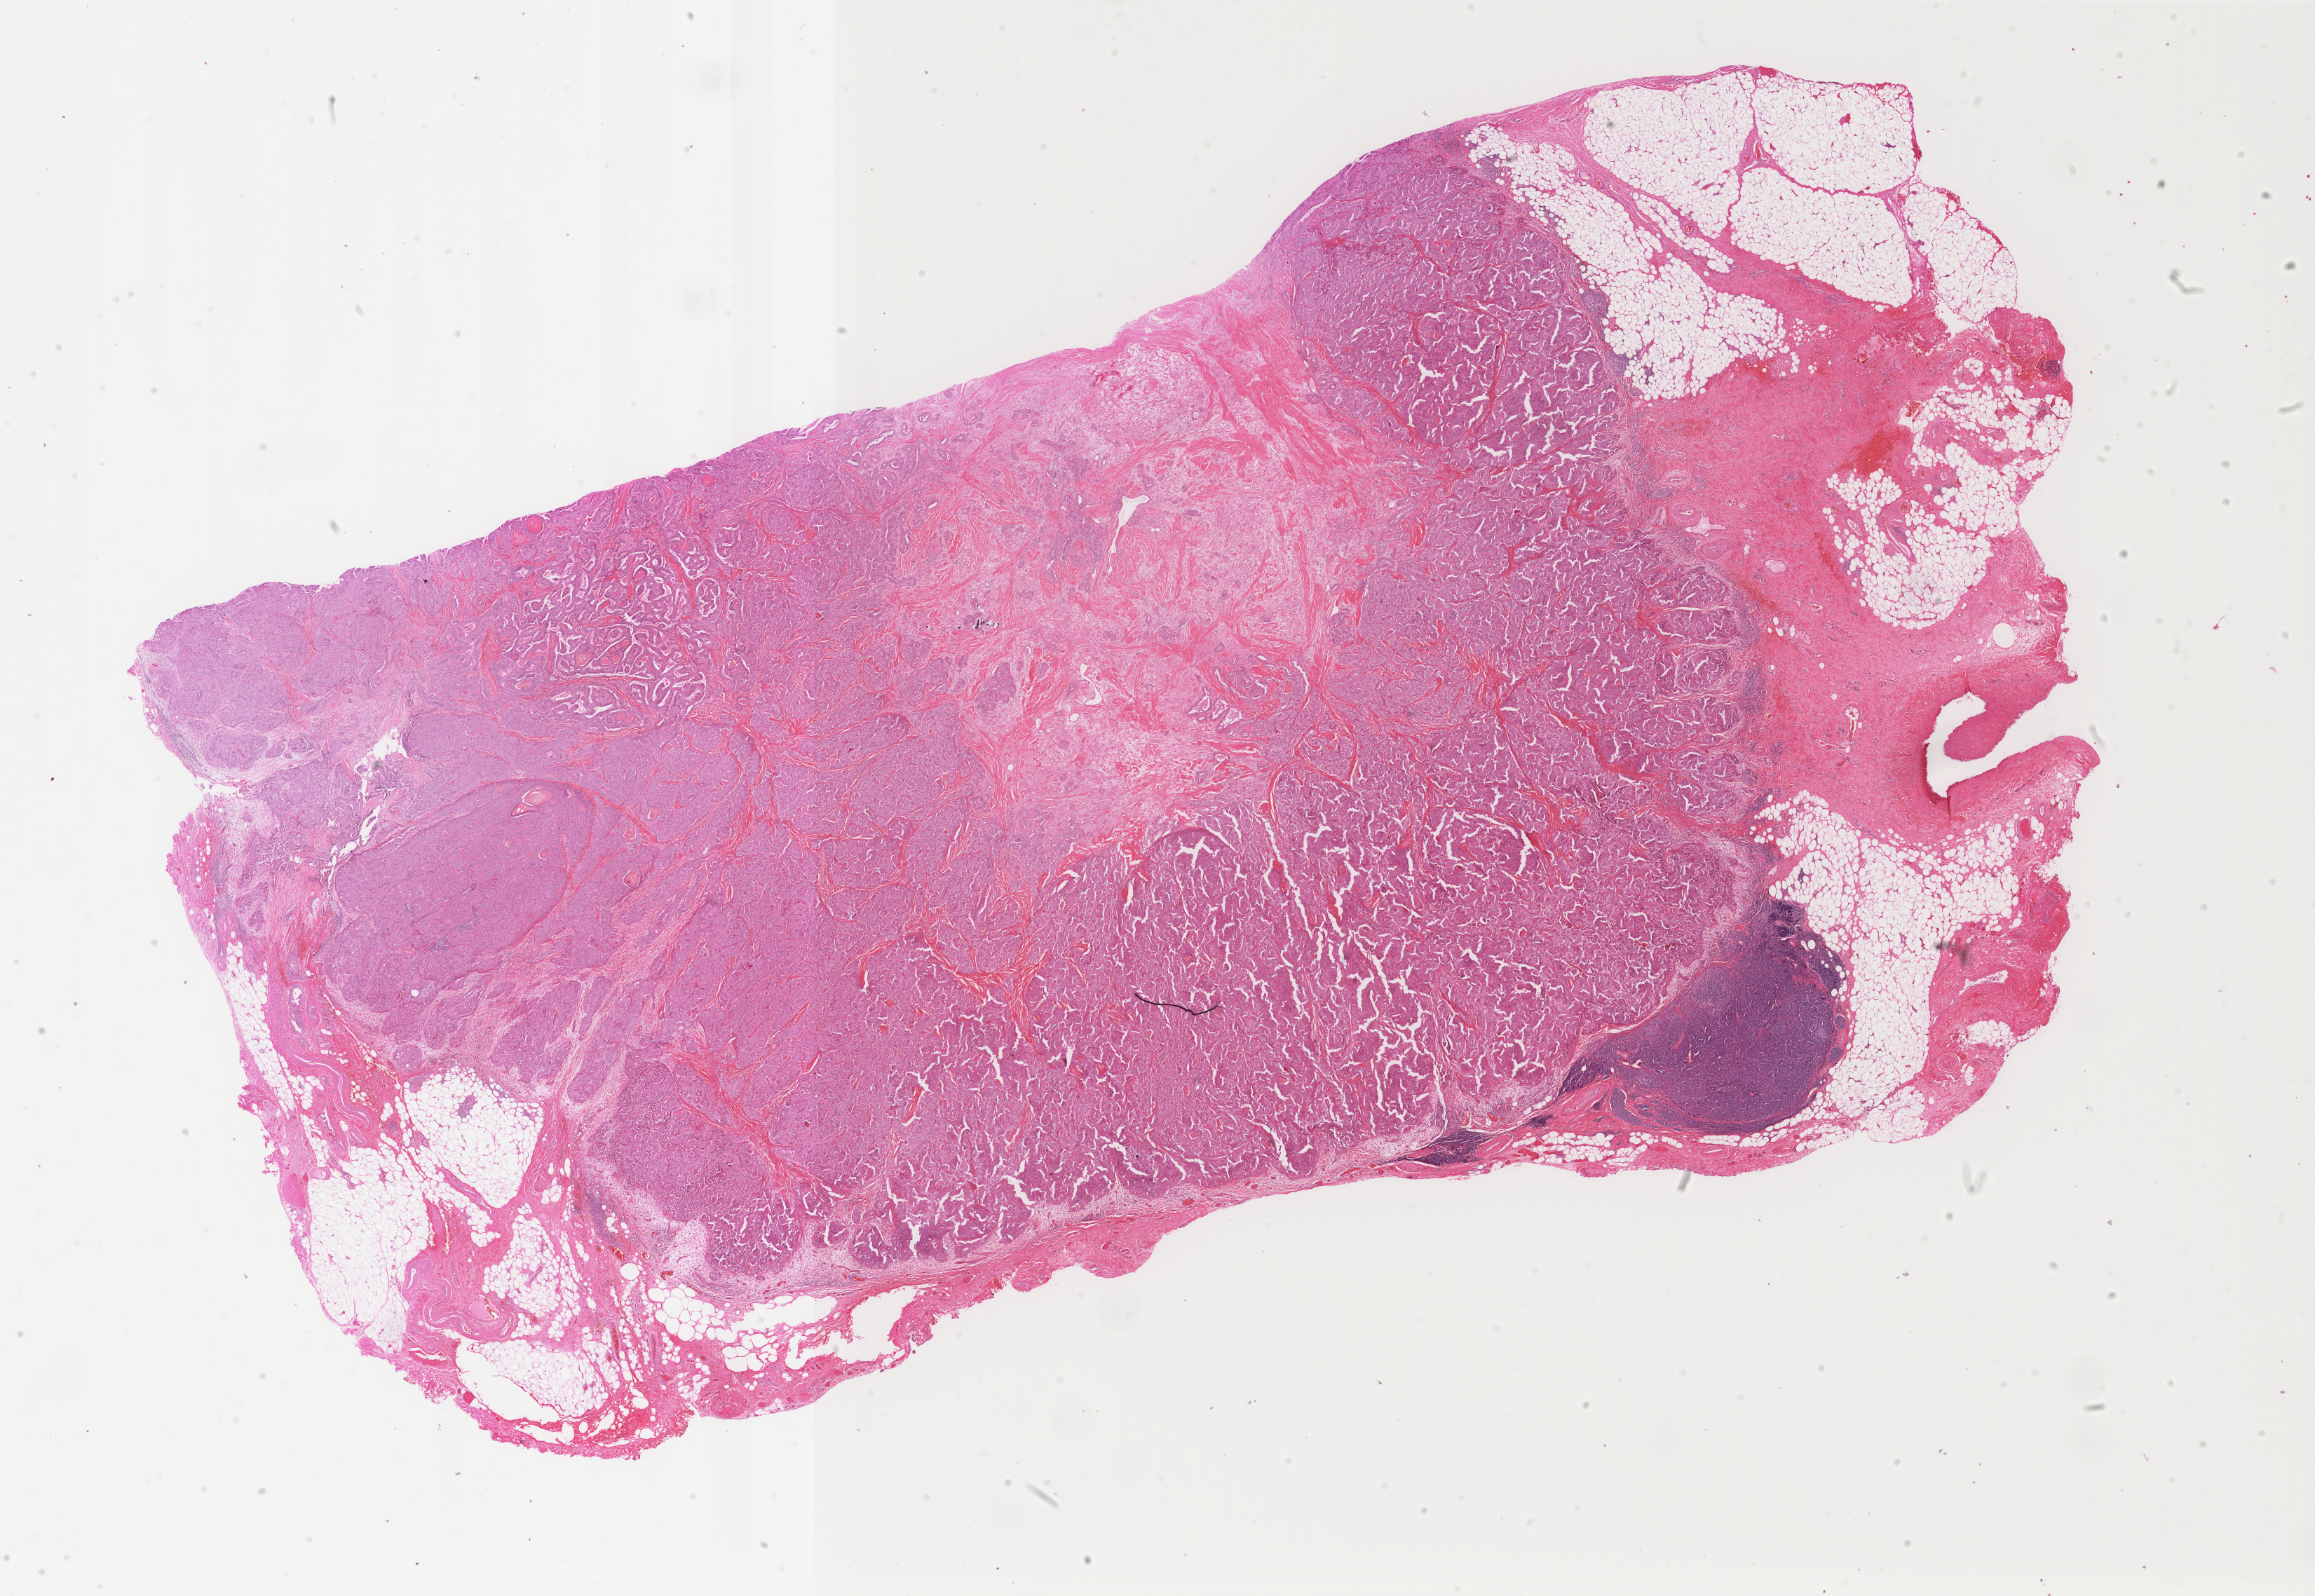
Whole-slide histology image, H&E-stained — a low-resolution overview of the entire scanned area, about 26.2 x 18.1 mm (from a 40x scan). Formalin-fixed paraffin-embedded (FFPE) diagnostic section. Sample: primary tumour, thyroid. Female patient; age at initial diagnosis 72 years.
Pathologic diagnosis: Papillary adenocarcinoma, NOS (thyroid gland).